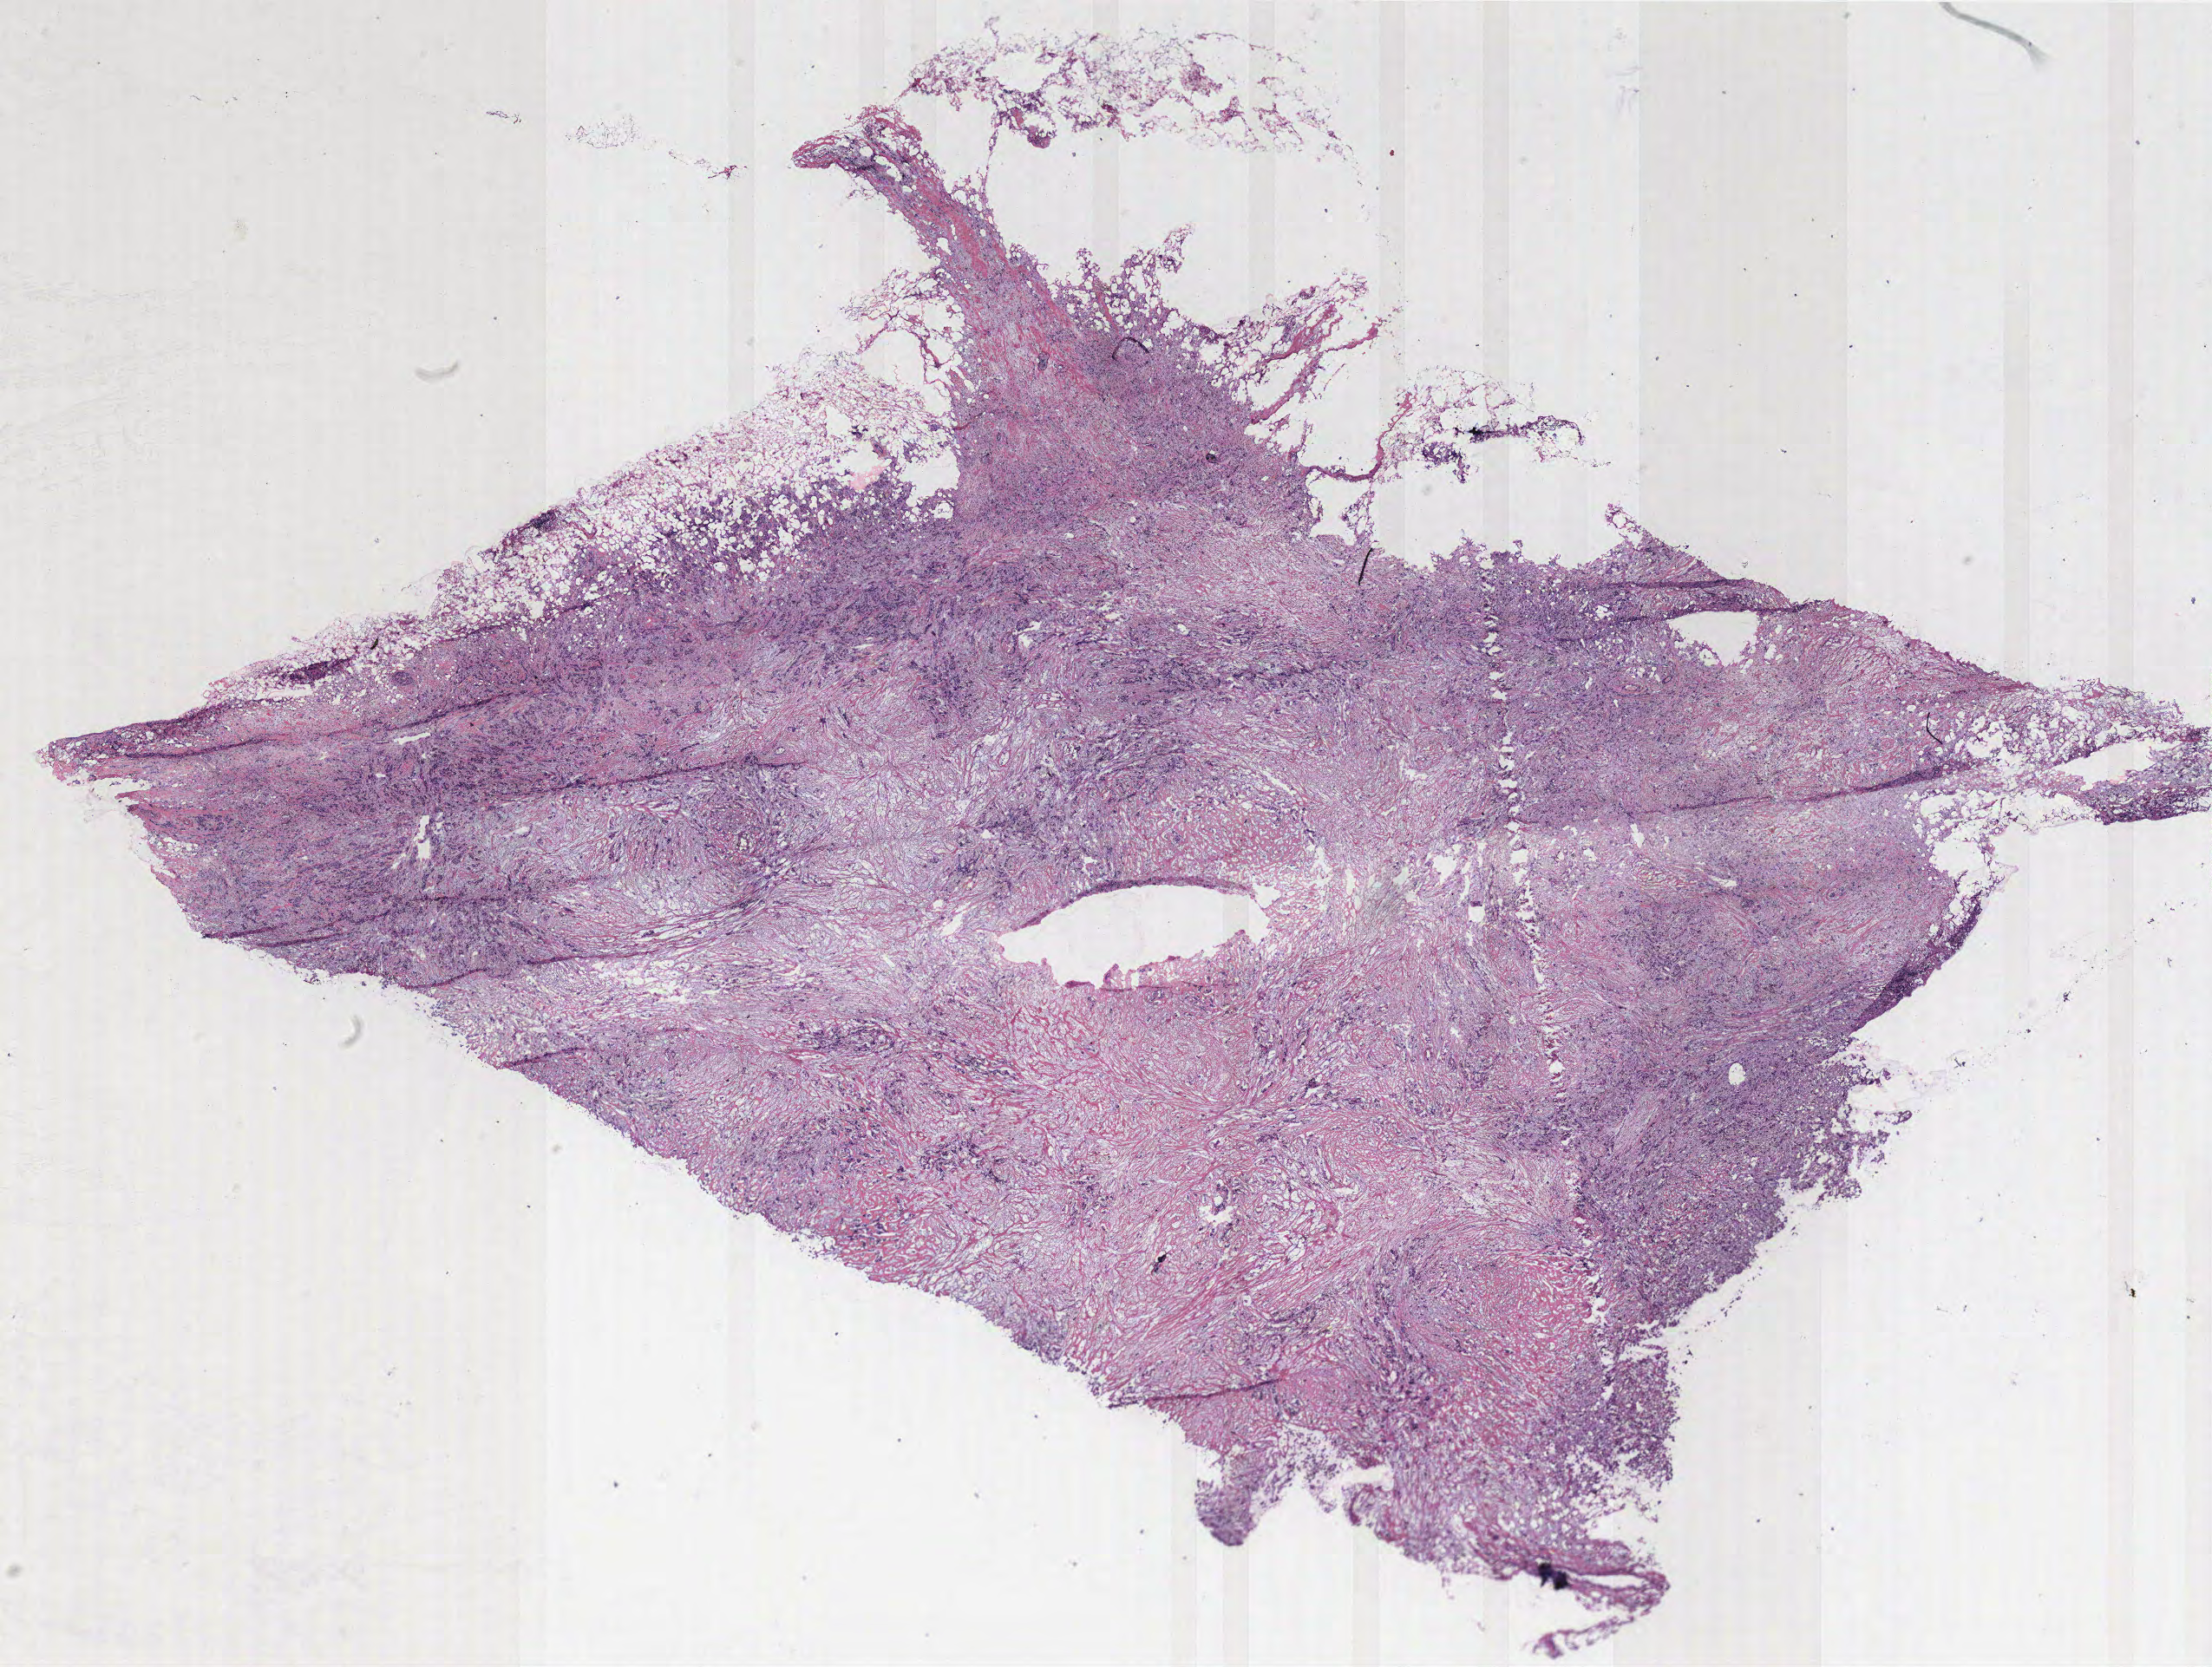
Whole-slide histology image, Hematoxylin and eosin (H&E) stained — whole scanned area (about 20.4 x 15.4 mm, acquisition: 40x scan) shown as a low-resolution overview. Breast, tumour tissue. 56-year-old female patient.
Histologic diagnosis: Infiltrating duct carcinoma, NOS. AJCC pathologic stage: IIA.